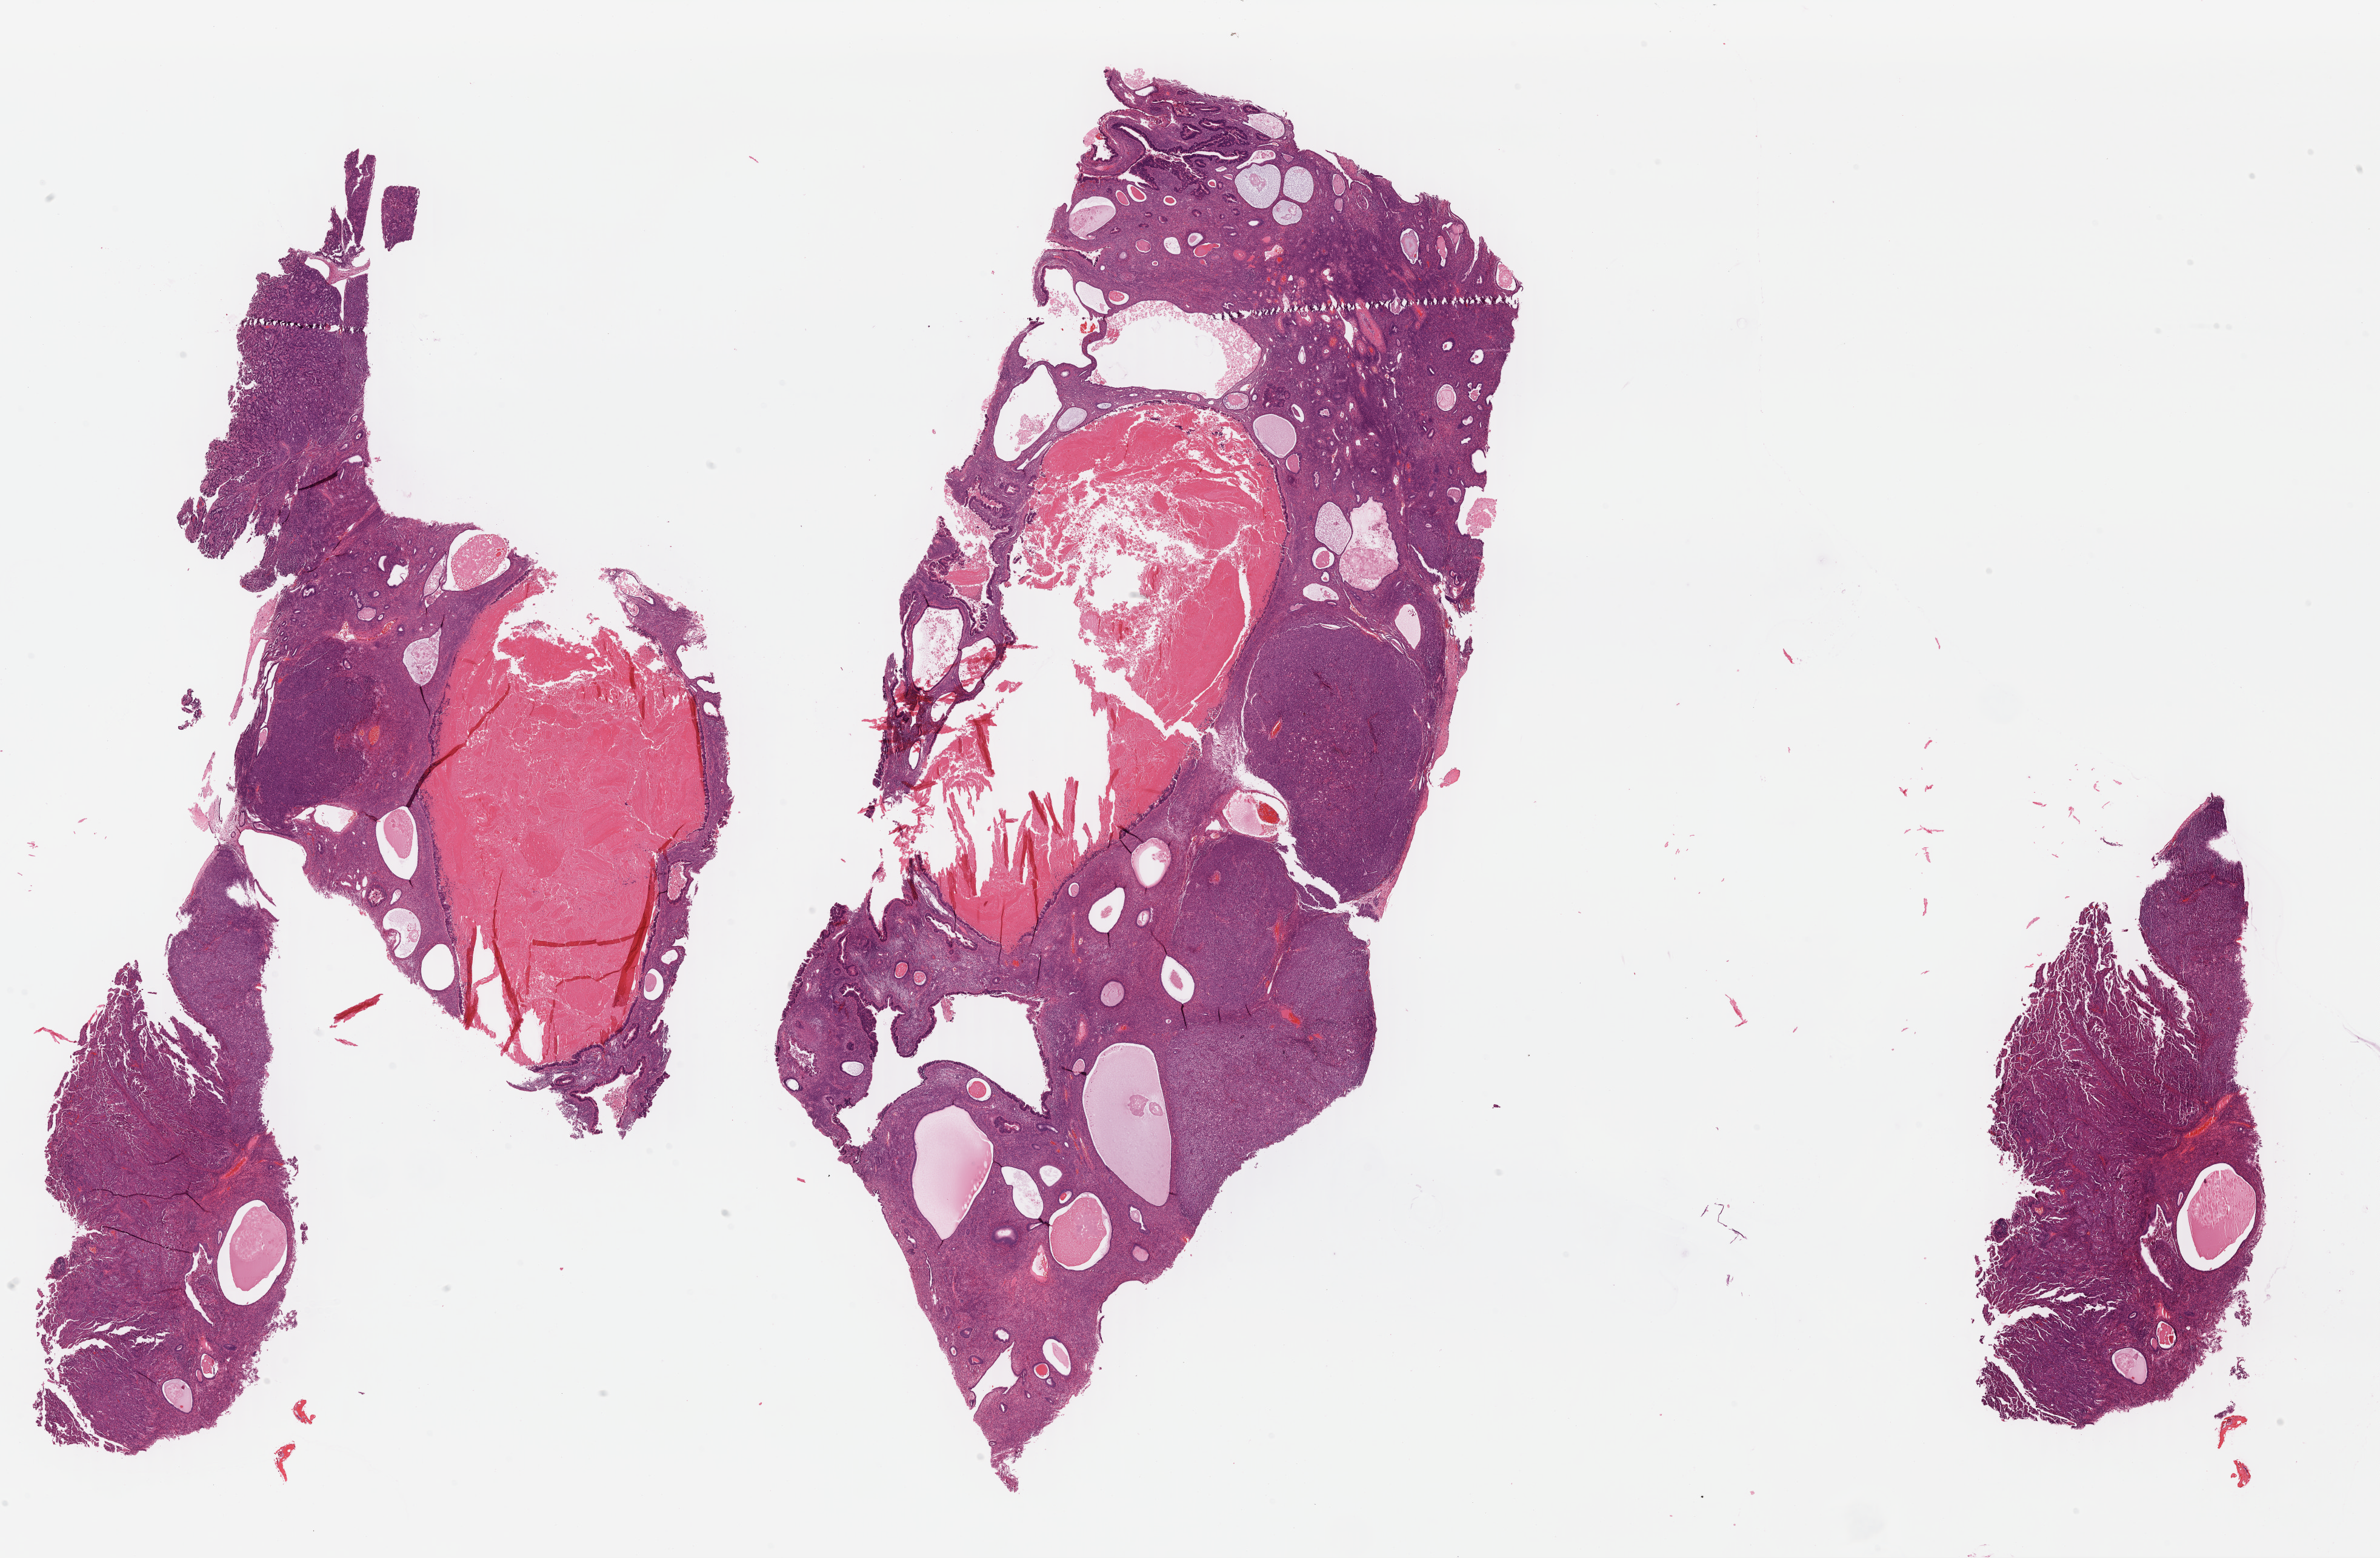
H&E-stained whole-slide image, whole scanned area (about 30.9 x 20.2 mm, from a 40x scan) shown as a low-resolution overview, FFPE section, primary tumour sample from the uterus. Patient: female, age at initial diagnosis 69 years.
Lymph nodes positive (case pathology): 0 of 5 examined. Diagnosis: Mullerian mixed tumor (endometrium). FIGO stage: IA.